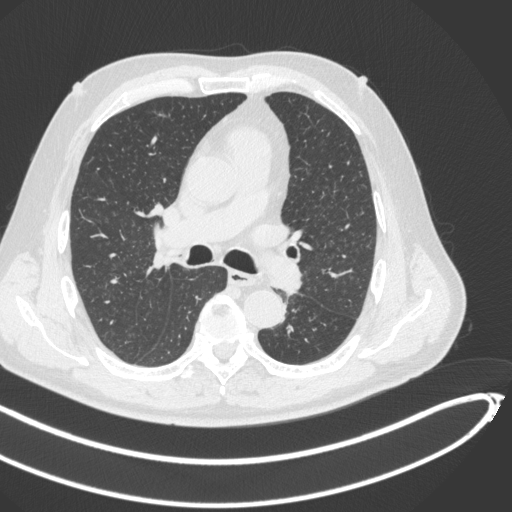
Chest CT, one axial slice; position 279 of 466 along the scan axis; reconstruction kernel B31f; lung window (W 1500 / L -600 HU); 1 mm slice thickness; 512 × 512 image matrix, field of view 400 × 400 mm. Patient: male, 64 years. From the clinical record (not read from this slice): clinical TNM (as recorded): T1c N0 M0; histopathological grade: G2.
Annotated regions visible in this slice (bounding box drawn by a radiologist):
- lung tumour (recorded histology: squamous cell carcinoma): bounding box (x1, y1, x2, y2) in pixels: (258, 245, 305, 299)